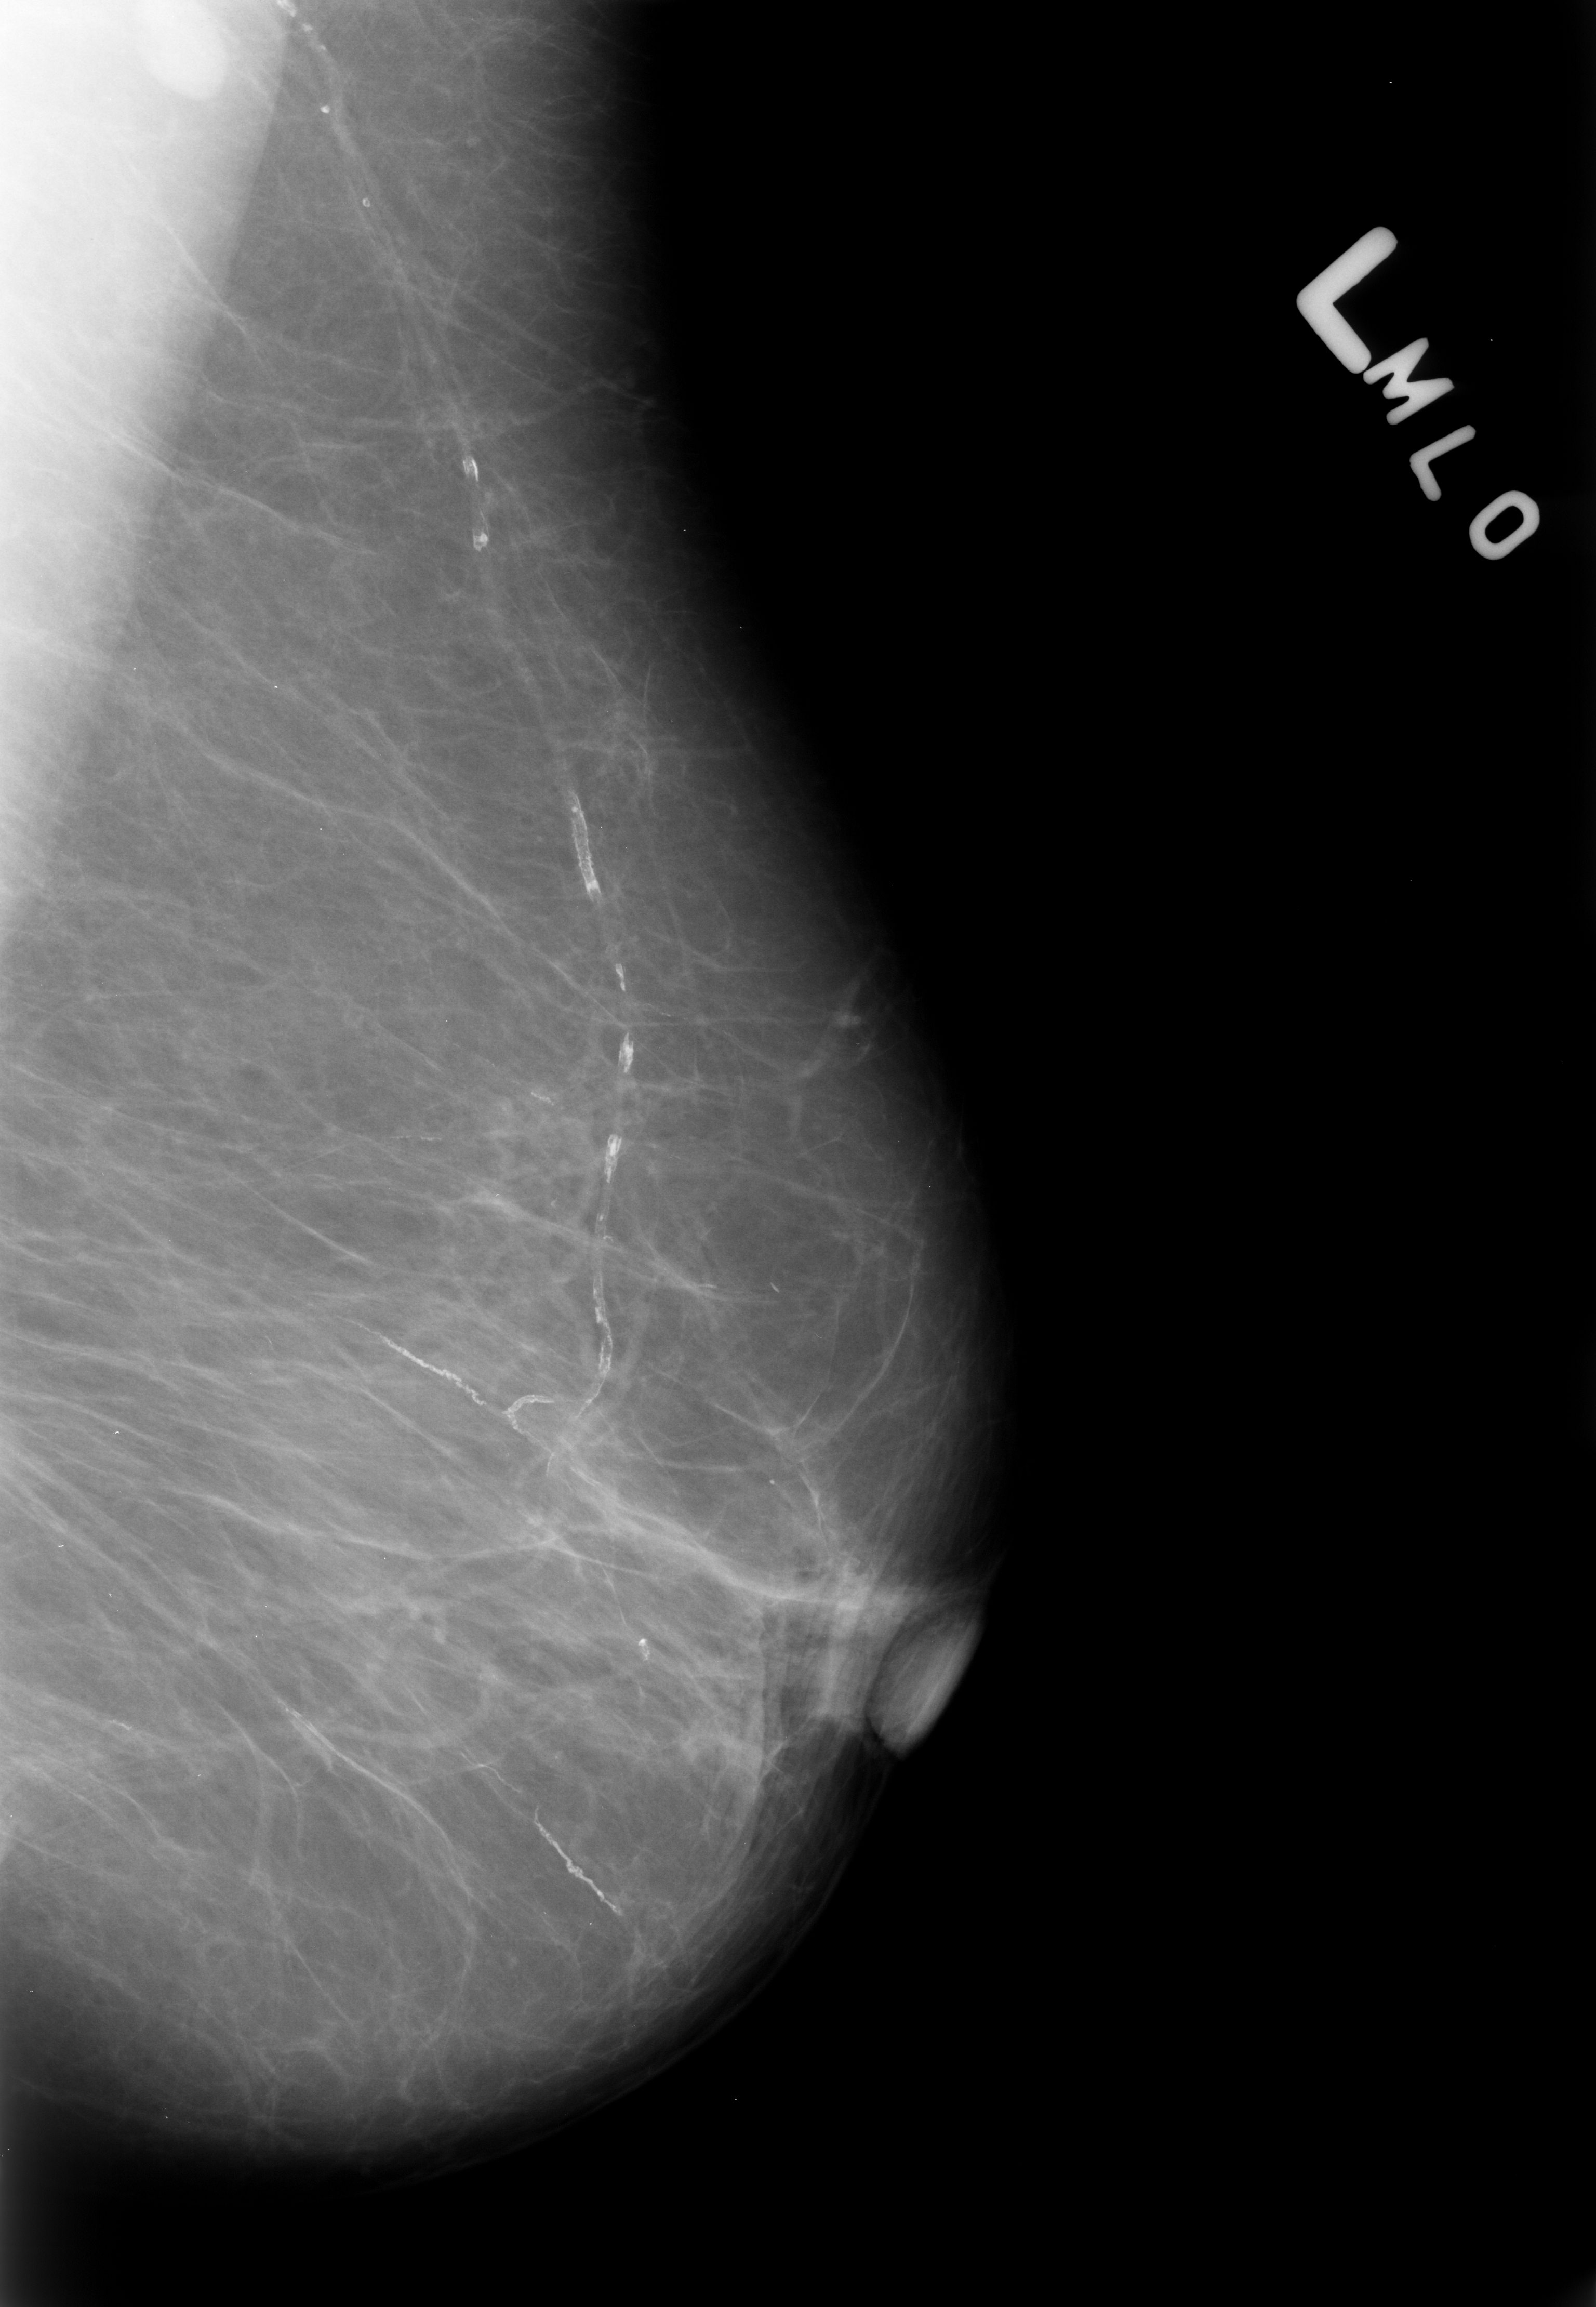
Scanned film-screen mammogram, left breast, MLO view, BI-RADS breast density category 1 (scale 1–4).
- Radiologist-marked abnormalities on this image: Finding 1 of 2: calcifications, morphology vascular; BI-RADS assessment category 2; subtlety rating 5 on a 1 (subtle) to 5 (obvious) scale; benign without callback (not worked up further).
- Finding 2 of 2: calcifications, morphology vascular; BI-RADS assessment category 2; benign without callback (not worked up further).